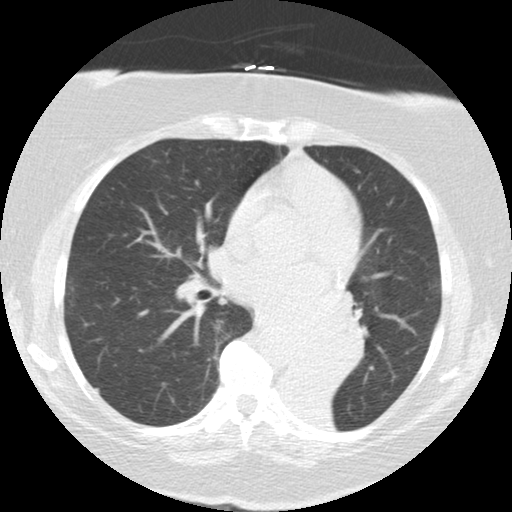
Low-dose screening chest CT, axial slice, baseline screening round, lung window (W 1500 / L -600 HU). Female, age 71 years at enrolment. Former smoker at enrolment.
Lesion marked by an expert reader, bounding box <285,306,366,383> (left, top, right, bottom; pixels). Reader record for this screening exam (exam-level; its link to the box is not recorded): non-calcified nodule or mass ≥4 mm, right middle lobe, 5 × 5 mm, smooth margins, soft tissue attenuation. Note: the box lies in the patient's left hemithorax on this image, whereas the reader's record names the right lung; they may be different findings. Lung cancer was diagnosed 46 days after this screen: large cell carcinoma, NOS, left lower lobe, mediastinum, other location, poorly differentiated (G3), stage IV (AJCC 6th edition), 50 mm at pathology.